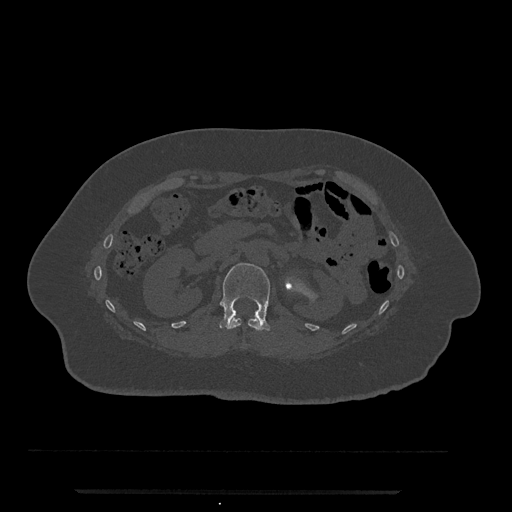
CT including the spine, one axial slice. Position 123 of 797 along the scan axis. Bone window (W 1800 / L 400 HU). 512 × 512 image matrix, field of view 440 × 440 mm. Female patient, age 51 years. From the clinical record (not read from this slice): primary cancer: neuro; vertebrae with lytic lesions (as recorded): T8.
Annotated regions visible in this slice (semi-automatically segmented with operator editing):
- L1 vertebra: bounding box (x1, y1, x2, y2) in pixels: (219, 263, 270, 331)
- T12 vertebra: (227, 318, 262, 331)